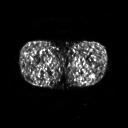
FDG PET of an extremity soft-tissue mass (from a PET/CT study), one axial slice. Position 229 of 267 along the scan axis. 3.27 mm slice thickness. 128 × 128 image matrix, field of view 500 × 500 mm. Male patient, age 27 years. Case-level facts recorded for this patient, not image findings: histological type: extraskeletal osteosarcoma; grade: high; site of the primary tumour: left adductur.
Structures marked on this image (expert contour drawn on MRI and transferred to this co-registered scan by the dataset authors):
- gross tumour volume (mass): box from (x=67, y=61) to (x=92, y=78) px